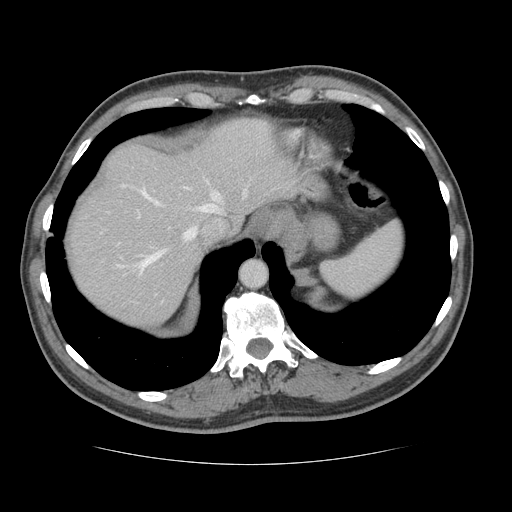
Contrast-enhanced abdominal CT, one axial slice; position 109 of 134 along the scan axis; reconstruction kernel STANDARD; intravenous contrast given; soft-tissue window (W 400 / L 40 HU); 2.5 mm slice thickness; 512 × 512 image matrix, field of view 377 × 377 mm. Male patient, age 68 years. From the clinical record (not read from this slice): diagnosis: colorectal cancer liver metastases, imaged before liver resection; multiple liver metastases: yes; largest metastasis: 2.2 cm; disease in both lobes: no.
Structures marked on this image (outlined manually by an expert reader):
- hepatic veins: bounding box (x1, y1, x2, y2) in pixels: (118, 186, 247, 274)
- liver: (69, 119, 290, 324)
- planned liver remnant (the part of the liver to remain after resection): (69, 119, 289, 311)